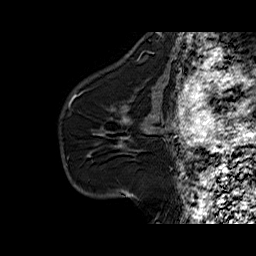
Breast MRI (dynamic contrast-enhanced), one sagittal slice; position 41 of 60 along the scan axis; dynamic contrast-enhanced series, time point 2 of 6 at this slice position (early post-contrast); 1.5 T; TE 6.3 ms, TR 32.5 ms; 4 mm slice thickness; 256 × 256 image matrix, field of view 200 × 200 mm. Female patient. From the clinical record (not read from this slice): setting: breast cancer imaged before/during neoadjuvant chemotherapy; receptor status: HR-positive, HER2-negative.
Structures marked on this image (semi-automatic segmentation, software-assisted and operator-edited):
- analysis volume of interest (the breast-tissue region the enhancement analysis was run in; not a lesion): bounding box (x1, y1, x2, y2) in pixels: (94, 103, 161, 161)
- tumour enhancement mask (voxels above the 100 % enhancement threshold inside the analysis volume of interest): (122, 120, 125, 139)